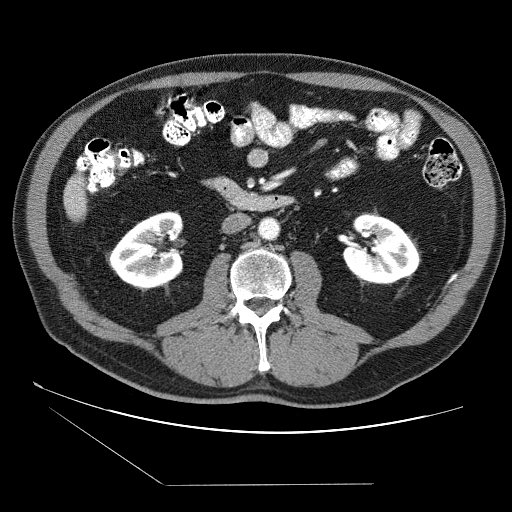
Contrast-enhanced abdominal CT (liver protocol), one axial slice. Reconstruction kernel STANDARD. 120 kVp. Soft-tissue window (W 400 / L 40 HU). 512 × 512 image matrix, field of view 400 × 400 mm. Case-level facts recorded for this patient, not image findings: diagnosis: hepatocellular carcinoma (patient treated with transarterial chemoembolisation; whether this scan precedes or follows treatment is not stated here); TNM stage (as recorded): Stage-II; Child-Pugh class: B.
Annotated regions visible in this slice (semi-automatic segmentation, software-assisted and operator-edited):
- liver parenchyma outside the tumour (the mass and vessels are separate outlines, so this box may not span the whole liver): bounding box <64,174,86,220> (left, top, right, bottom; pixels)